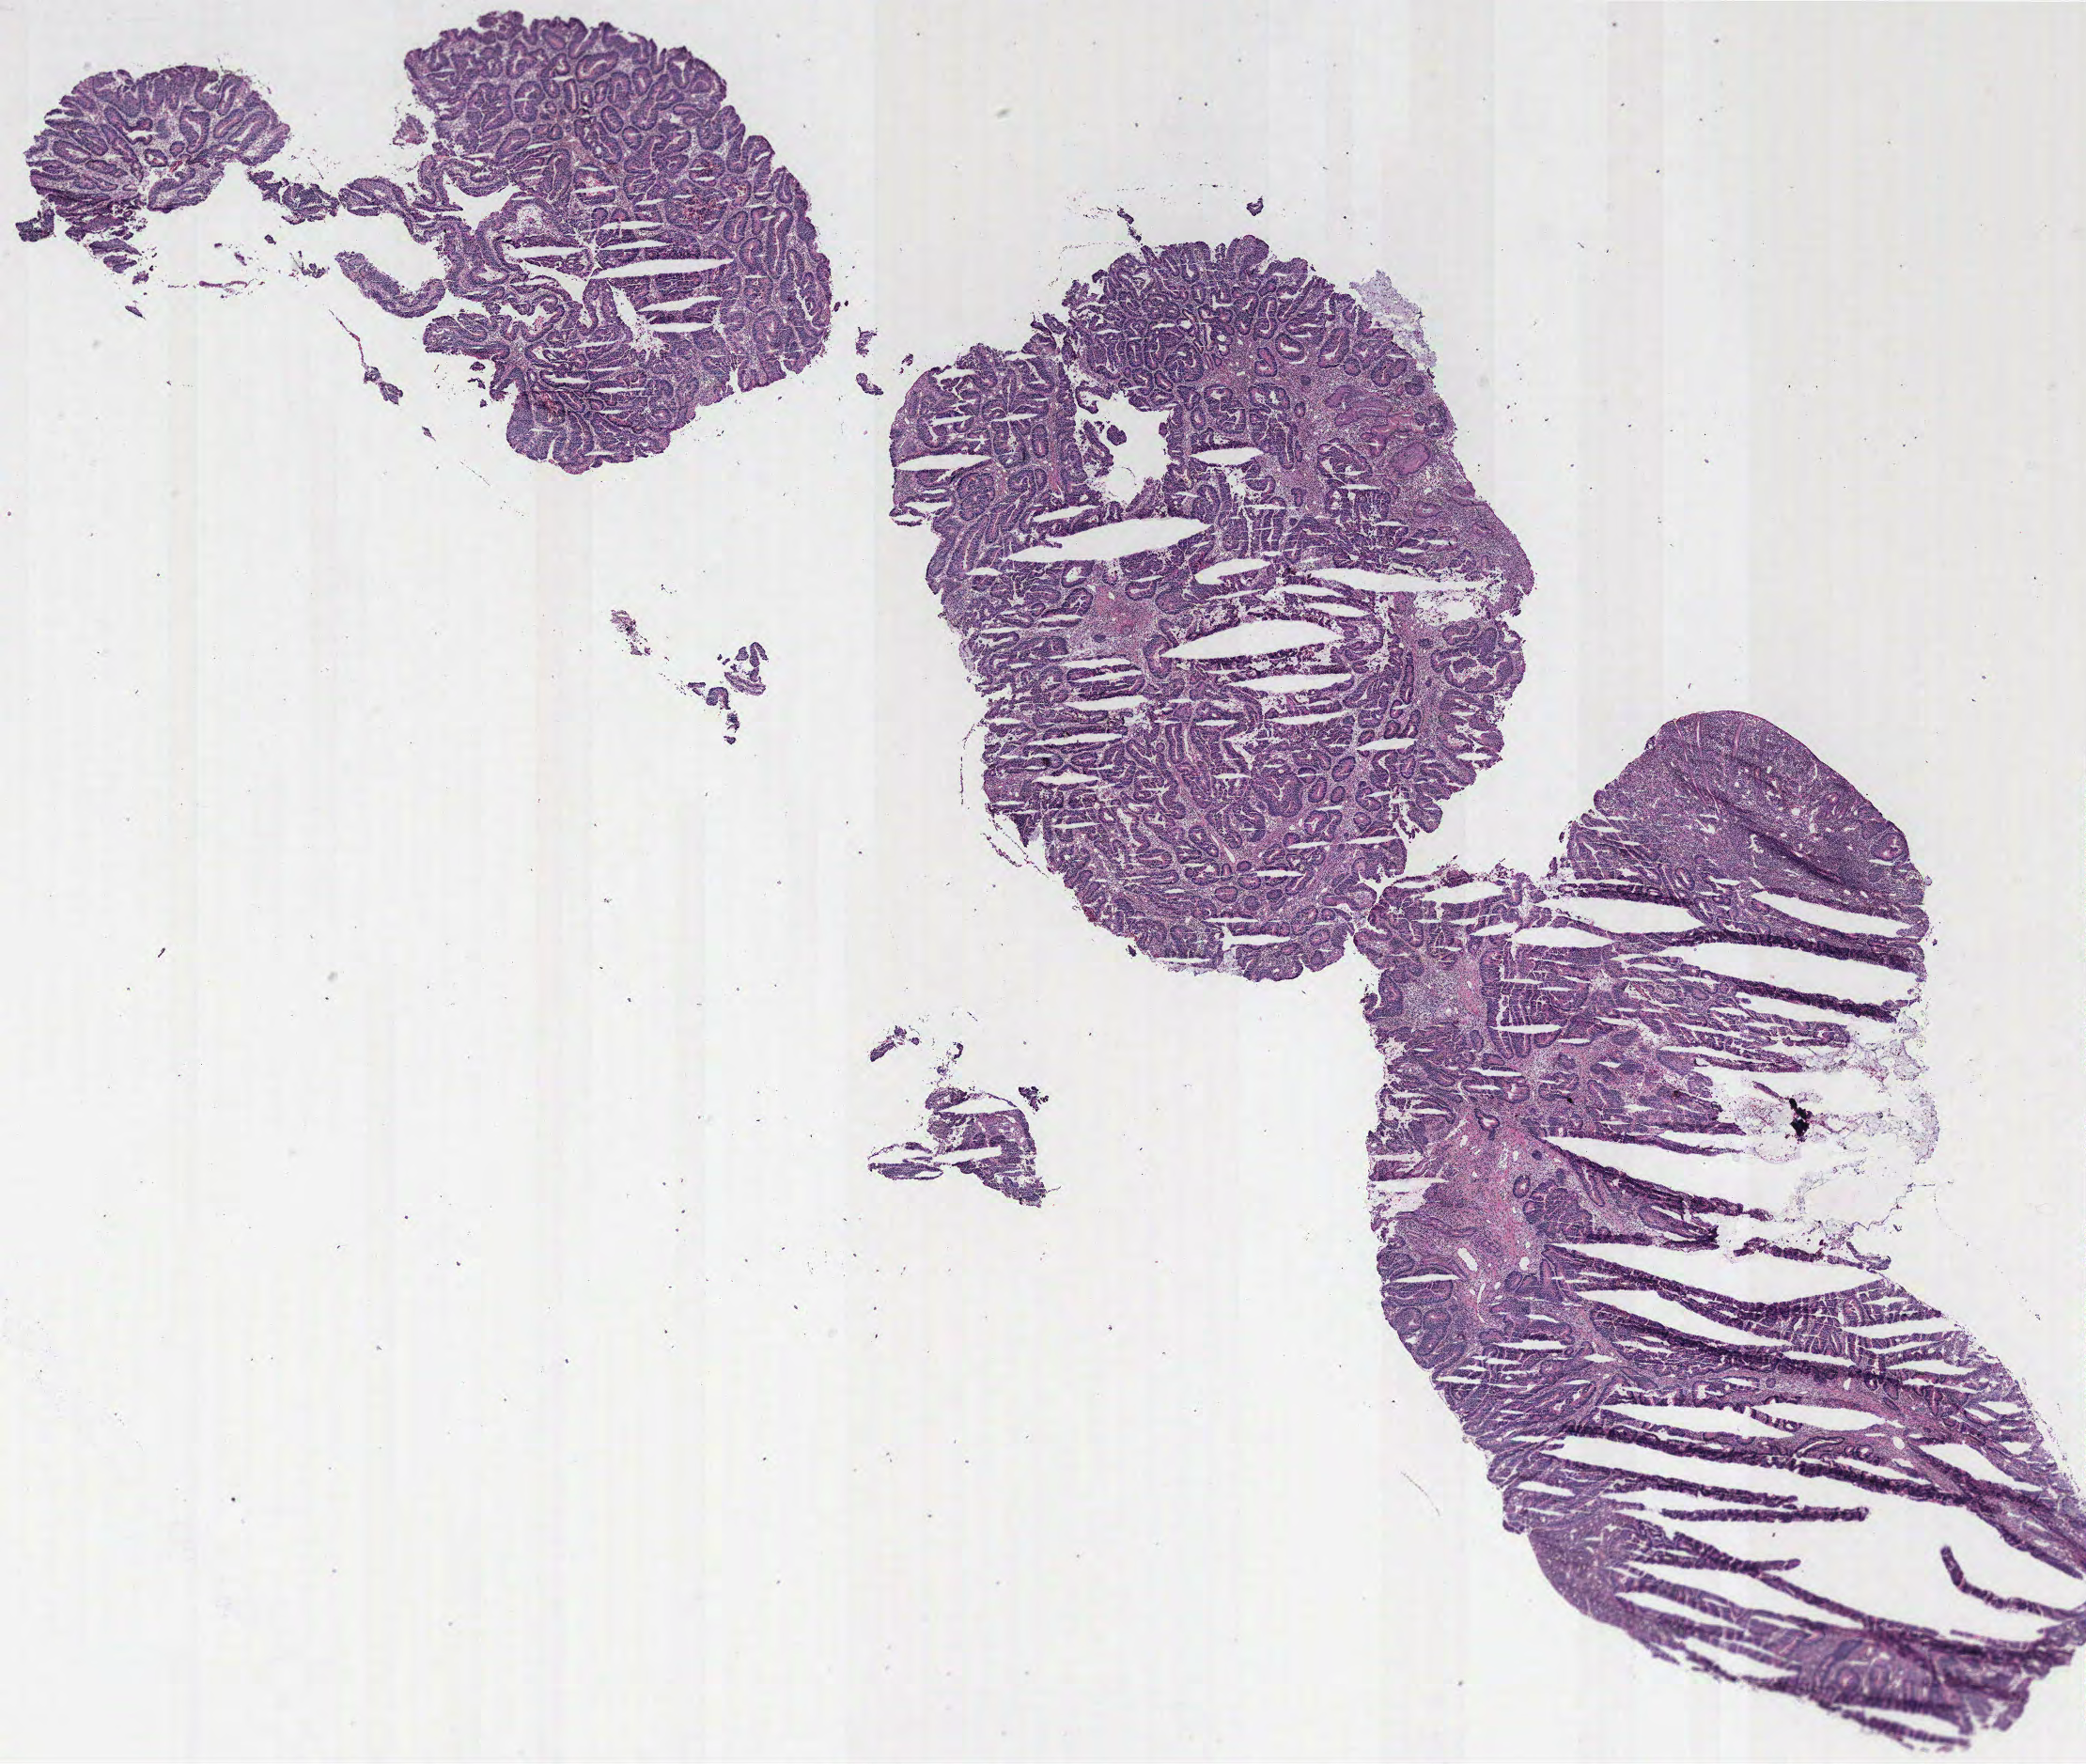
Digitized H&E tissue section (whole slide), whole scanned area (about 17.8 x 15.0 mm, slide scanned at 40x) shown as a low-resolution overview; colon, tissue type not recorded.
Patient diagnosis (cohort enrolment): colon cancer (colon).